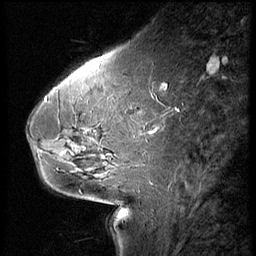
Breast MRI (dynamic contrast-enhanced), one sagittal slice; slice 22 of 66 in the series (ordered by position); 3 images stored at this slice position (order not interpretable as contrast timing); 1.5 T; TE 4.2 ms, TR 8.9 ms; 256 × 256 image matrix, field of view 200 × 200 mm. Patient: female, 54 years. Case-level facts recorded for this patient, not image findings: setting: breast cancer imaged before/during neoadjuvant chemotherapy; receptor status: HR-positive, HER2-negative.
Structures marked on this image (semi-automatic segmentation, software-assisted and operator-edited):
- analysis volume of interest (the breast-tissue region the enhancement analysis was run in; not a lesion): bounding box <61,104,146,171> (left, top, right, bottom; pixels)
- tumour enhancement mask (voxels above the 140 % enhancement threshold inside the analysis volume of interest): <110,106,142,167>